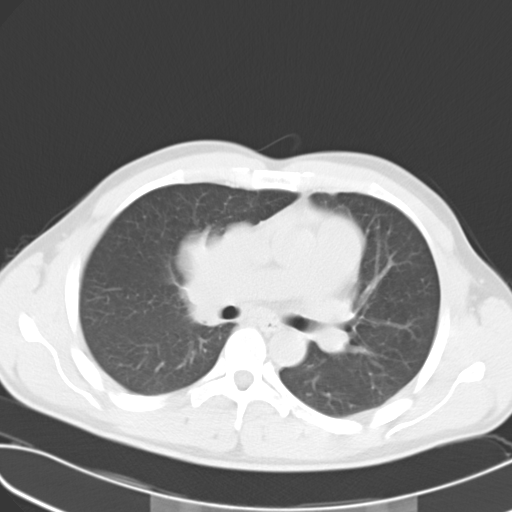
Chest CT, one axial slice. Slice 16 of 27 in the series (ordered by position). Lung window (W 1500 / L -600 HU). 10 mm slice thickness. 512 × 512 image matrix. Male patient, age 32 years. Case-level facts recorded for this patient, not image findings: clinical TNM (as recorded): T4 N3 M0; histopathological grade: G3.
Annotated regions visible in this slice (bounding box drawn by a radiologist):
- lung tumour (recorded histology: small cell carcinoma): box from (x=171, y=220) to (x=262, y=328) px